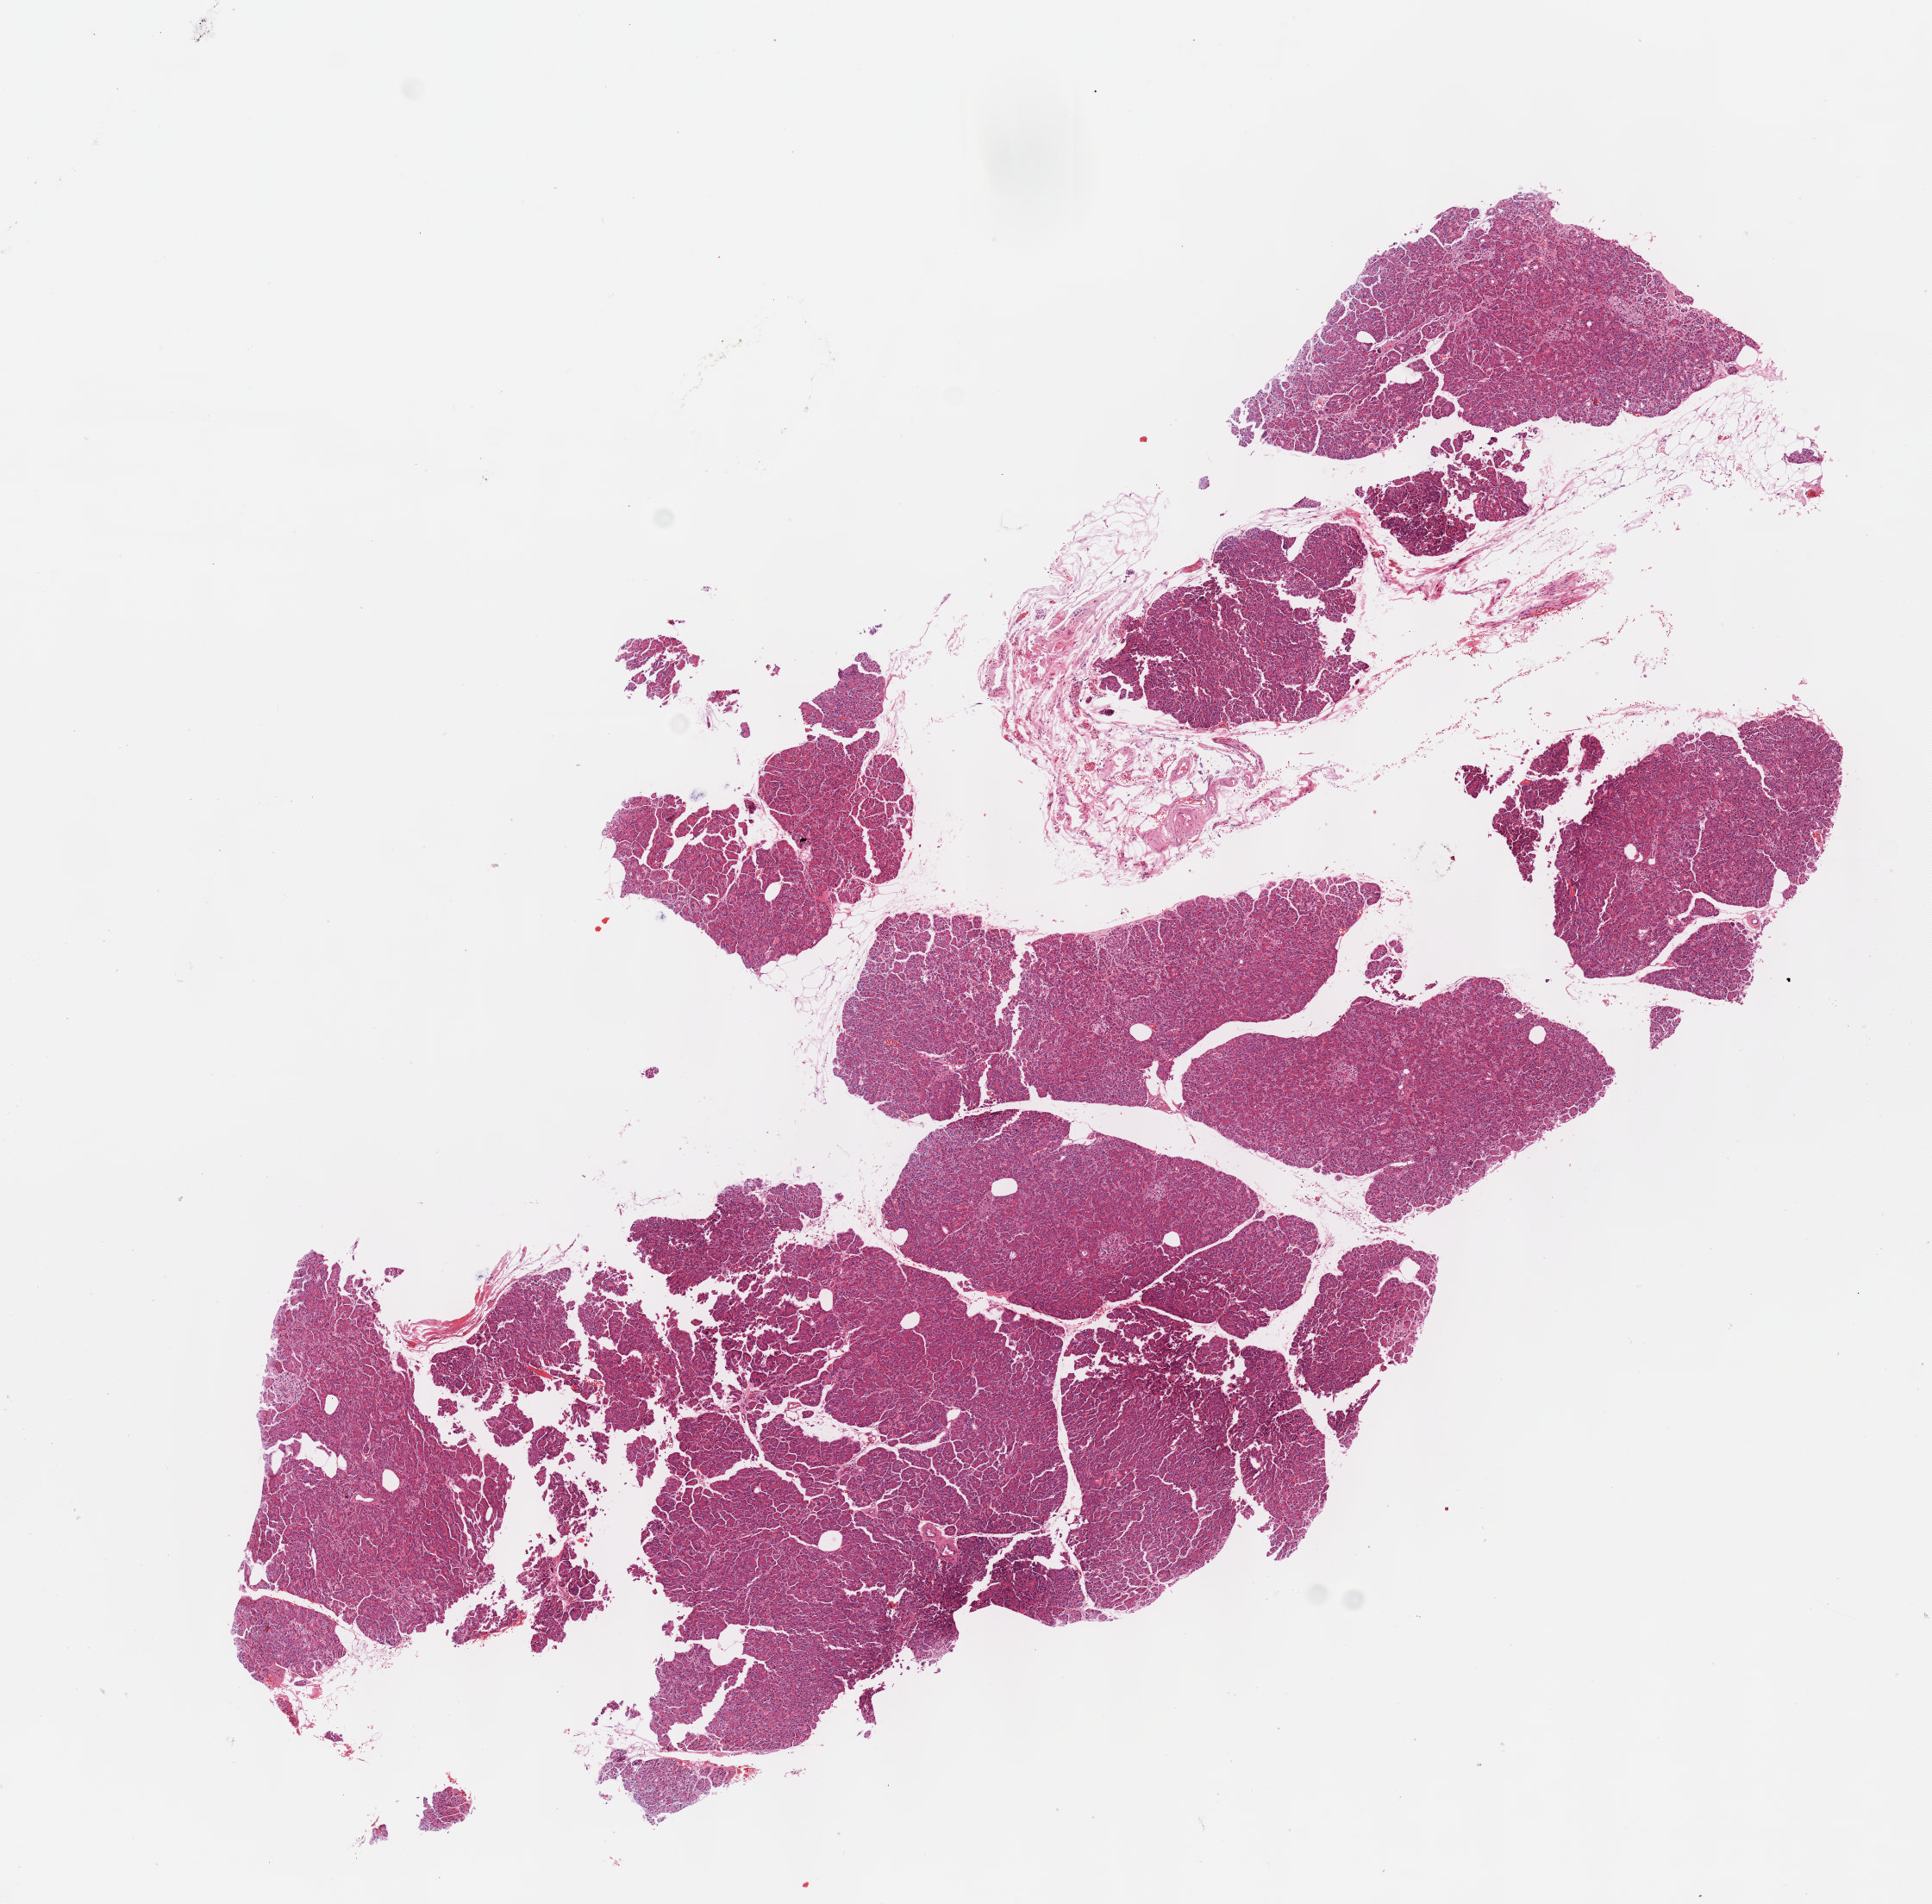
Digitized H&E-stained tissue section (whole slide), shown as a low-resolution overview of the whole scanned area (about 9.1 x 8.9 mm, from a 40x scan), FFPE section, sample: solid tissue normal (non-tumour tissue), pancreas. Patient: female, age at initial diagnosis 75 years.
This section: solid tissue normal (non-tumour) sample from the same patient. Patient diagnosis: Infiltrating duct carcinoma, NOS (body of pancreas).